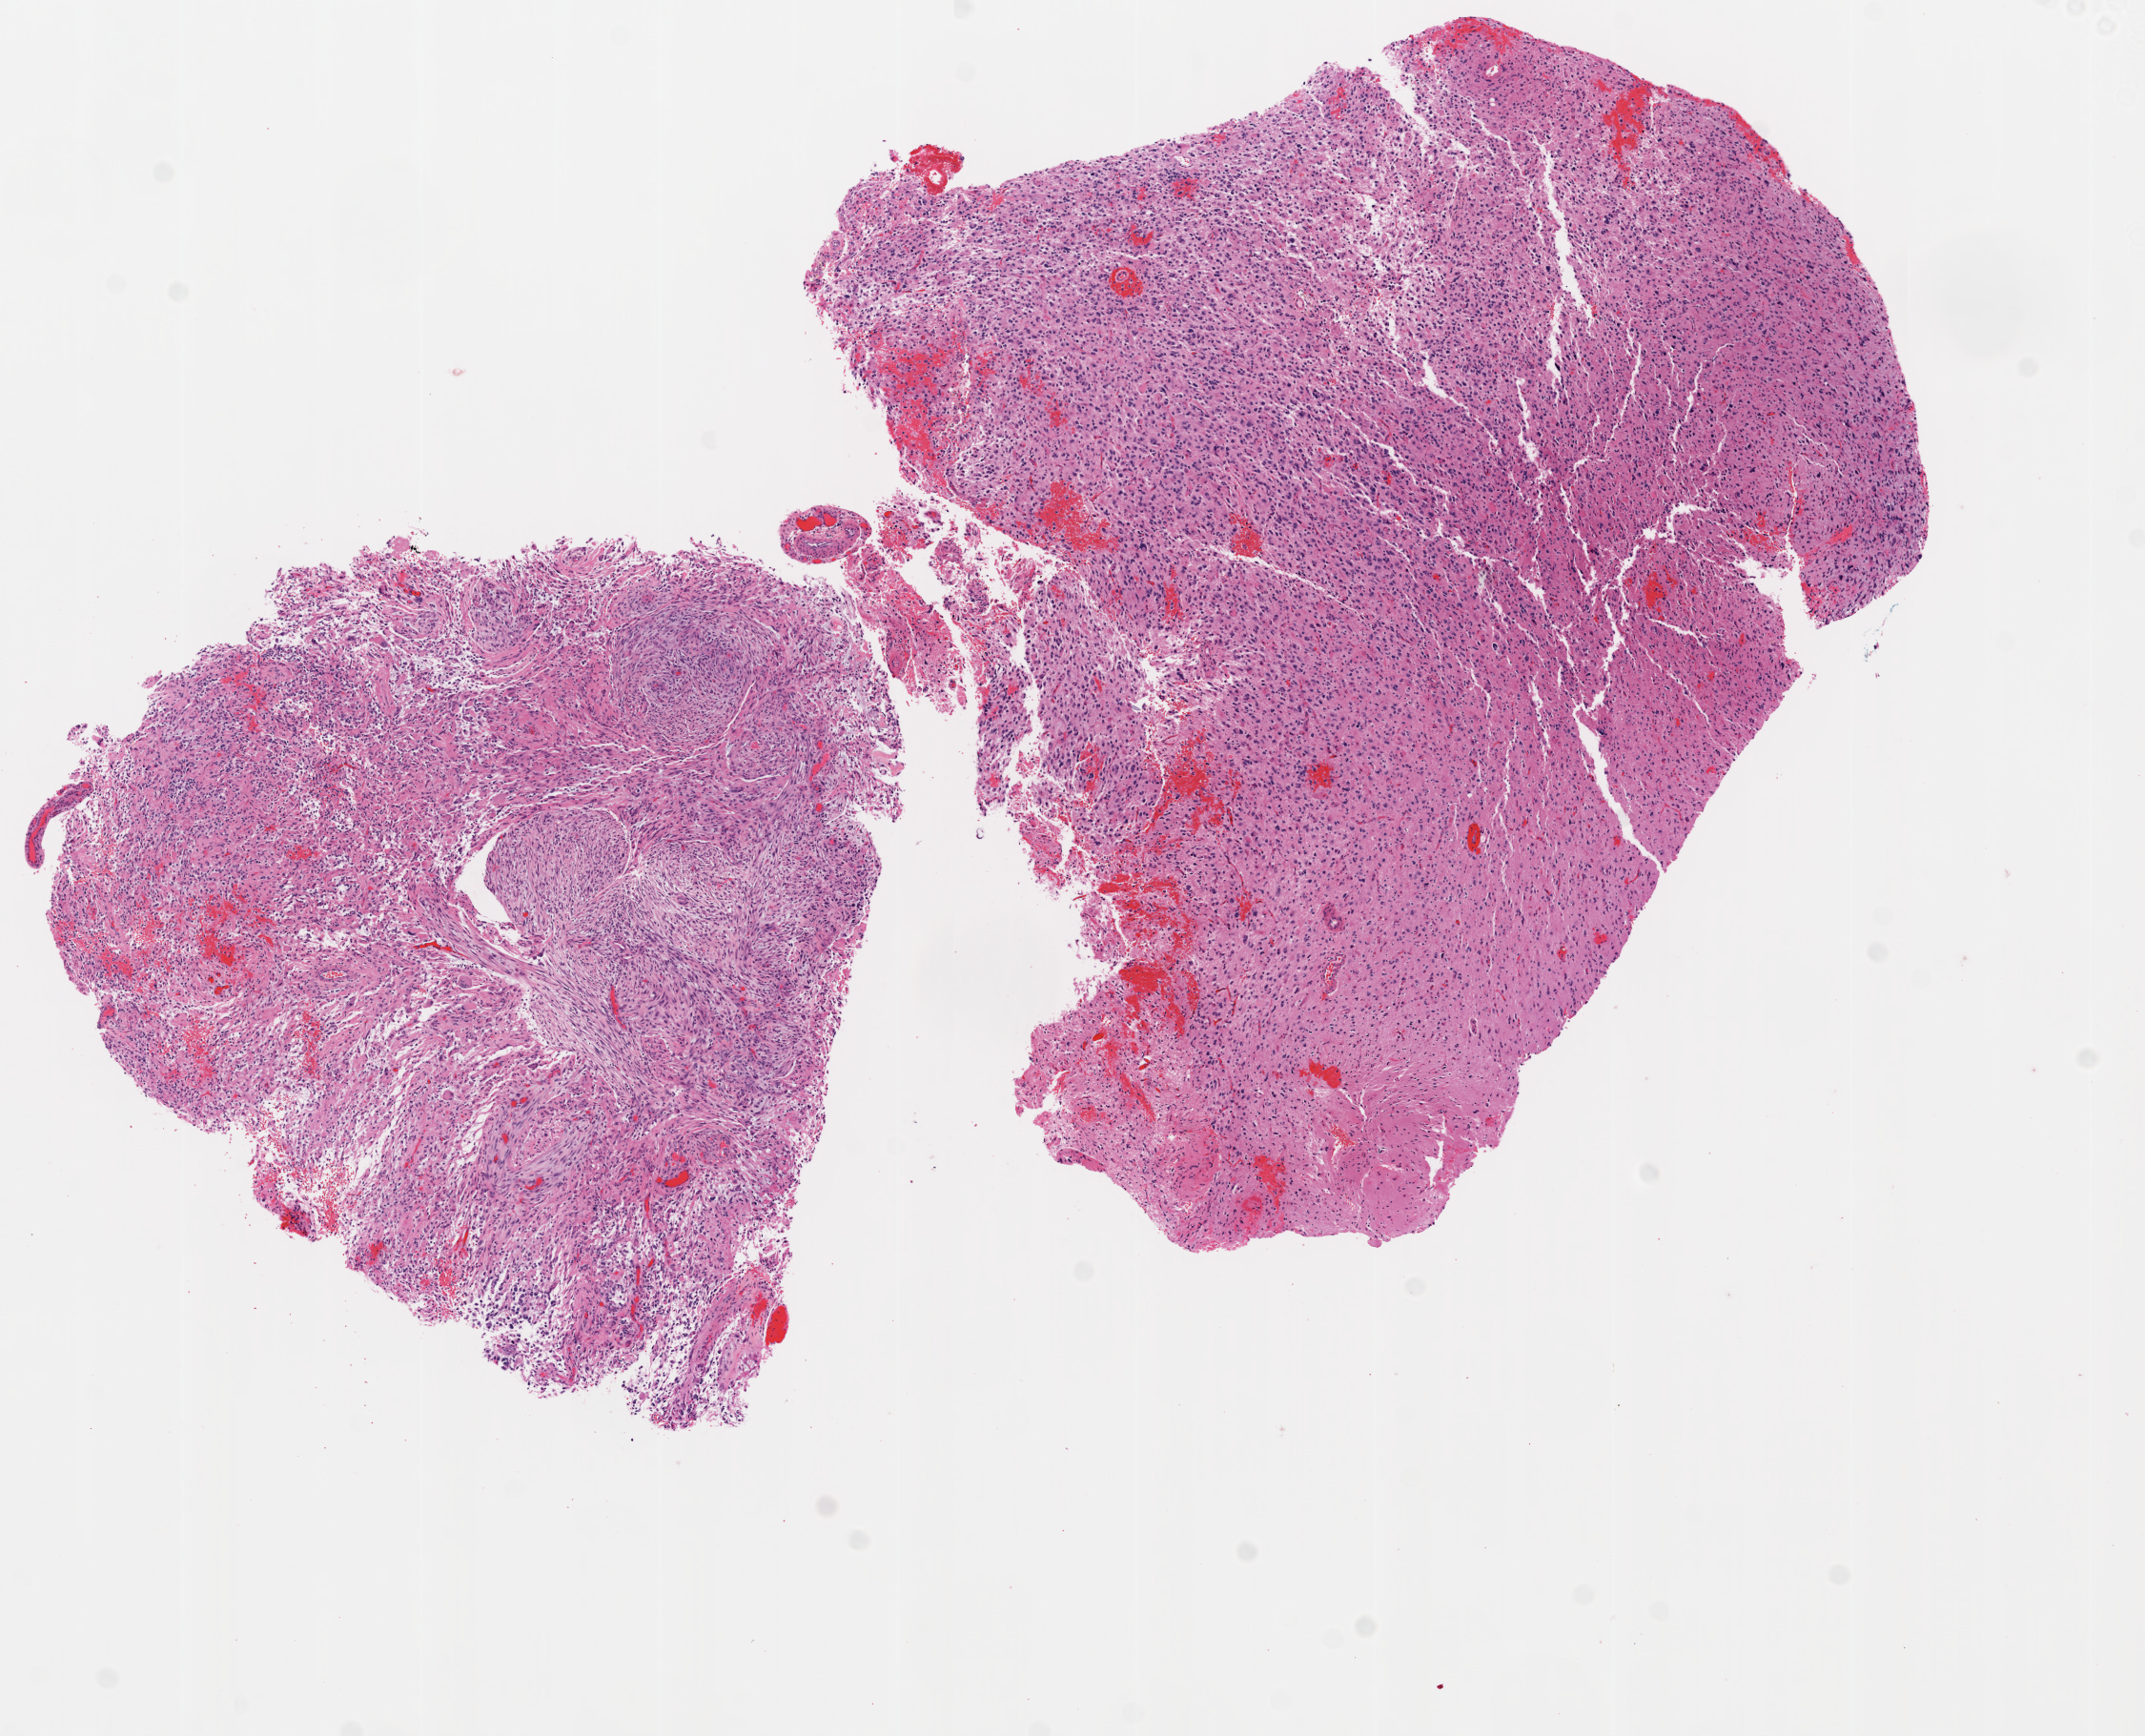
Digitized H&E-stained tissue section (whole slide) — whole scanned area (about 9.0 x 7.3 mm, acquisition: 20x scan) shown as a low-resolution overview. Frozen section from the top of the tissue portion. Sample: primary tumour, brain. Female patient; age at initial diagnosis 62 years. Pathologist review of this section (percent, as recorded): tumour cells 100%, tumour nuclei 80%, normal cells 0%, stromal cells 0%, necrosis 0%.
Diagnosis: Glioblastoma.